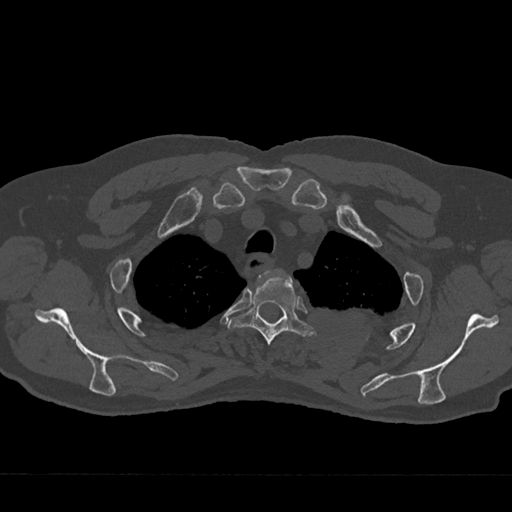
CT including the spine, one axial slice. Position 574 of 797 along the scan axis. Reconstruction kernel Br40s/3. Bone window (W 1800 / L 400 HU). 0.5 mm slice thickness. 512 × 512 image matrix. Patient: male, 75 years. From the clinical record (not read from this slice): primary cancer: renal; vertebrae with lytic lesions (as recorded): T4.
Annotated regions visible in this slice (semi-automatically segmented with operator editing):
- T2 vertebra: box from (x=259, y=271) to (x=271, y=278) px
- T3 vertebra: (x=229, y=274)–(x=316, y=345)